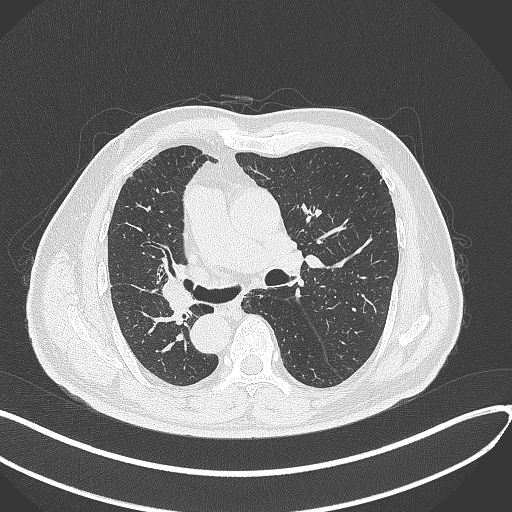
Chest CT, one axial slice; reconstruction kernel B70f; lung window (W 1500 / L -600 HU); 512 × 512 image matrix, field of view 400 × 400 mm. Male patient, age 67 years. Case-level facts recorded for this patient, not image findings: clinical TNM (as recorded): T2a N0 M0.
Annotated regions visible in this slice (rectangle marked by the reading radiologist):
- lung tumour (recorded histology: squamous cell carcinoma): bounding box [x1, y1, x2, y2] px = [160, 267, 196, 325]